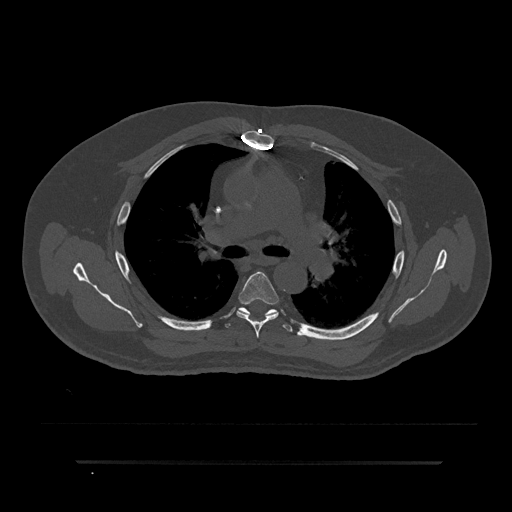
CT including the spine, one axial slice; position 561 of 797 along the scan axis; reconstruction kernel Br40s/3; 120 kVp; bone window (W 1800 / L 400 HU); 0.5 mm slice thickness; 512 × 512 image matrix. Male patient, age 59 years. Case-level facts recorded for this patient, not image findings: primary cancer: bile ducts.
Annotated regions visible in this slice (semi-automatically segmented with operator editing):
- T5 vertebra: bounding box [x1, y1, x2, y2] px = [236, 272, 279, 338]
- T6 vertebra: [225, 300, 294, 332]